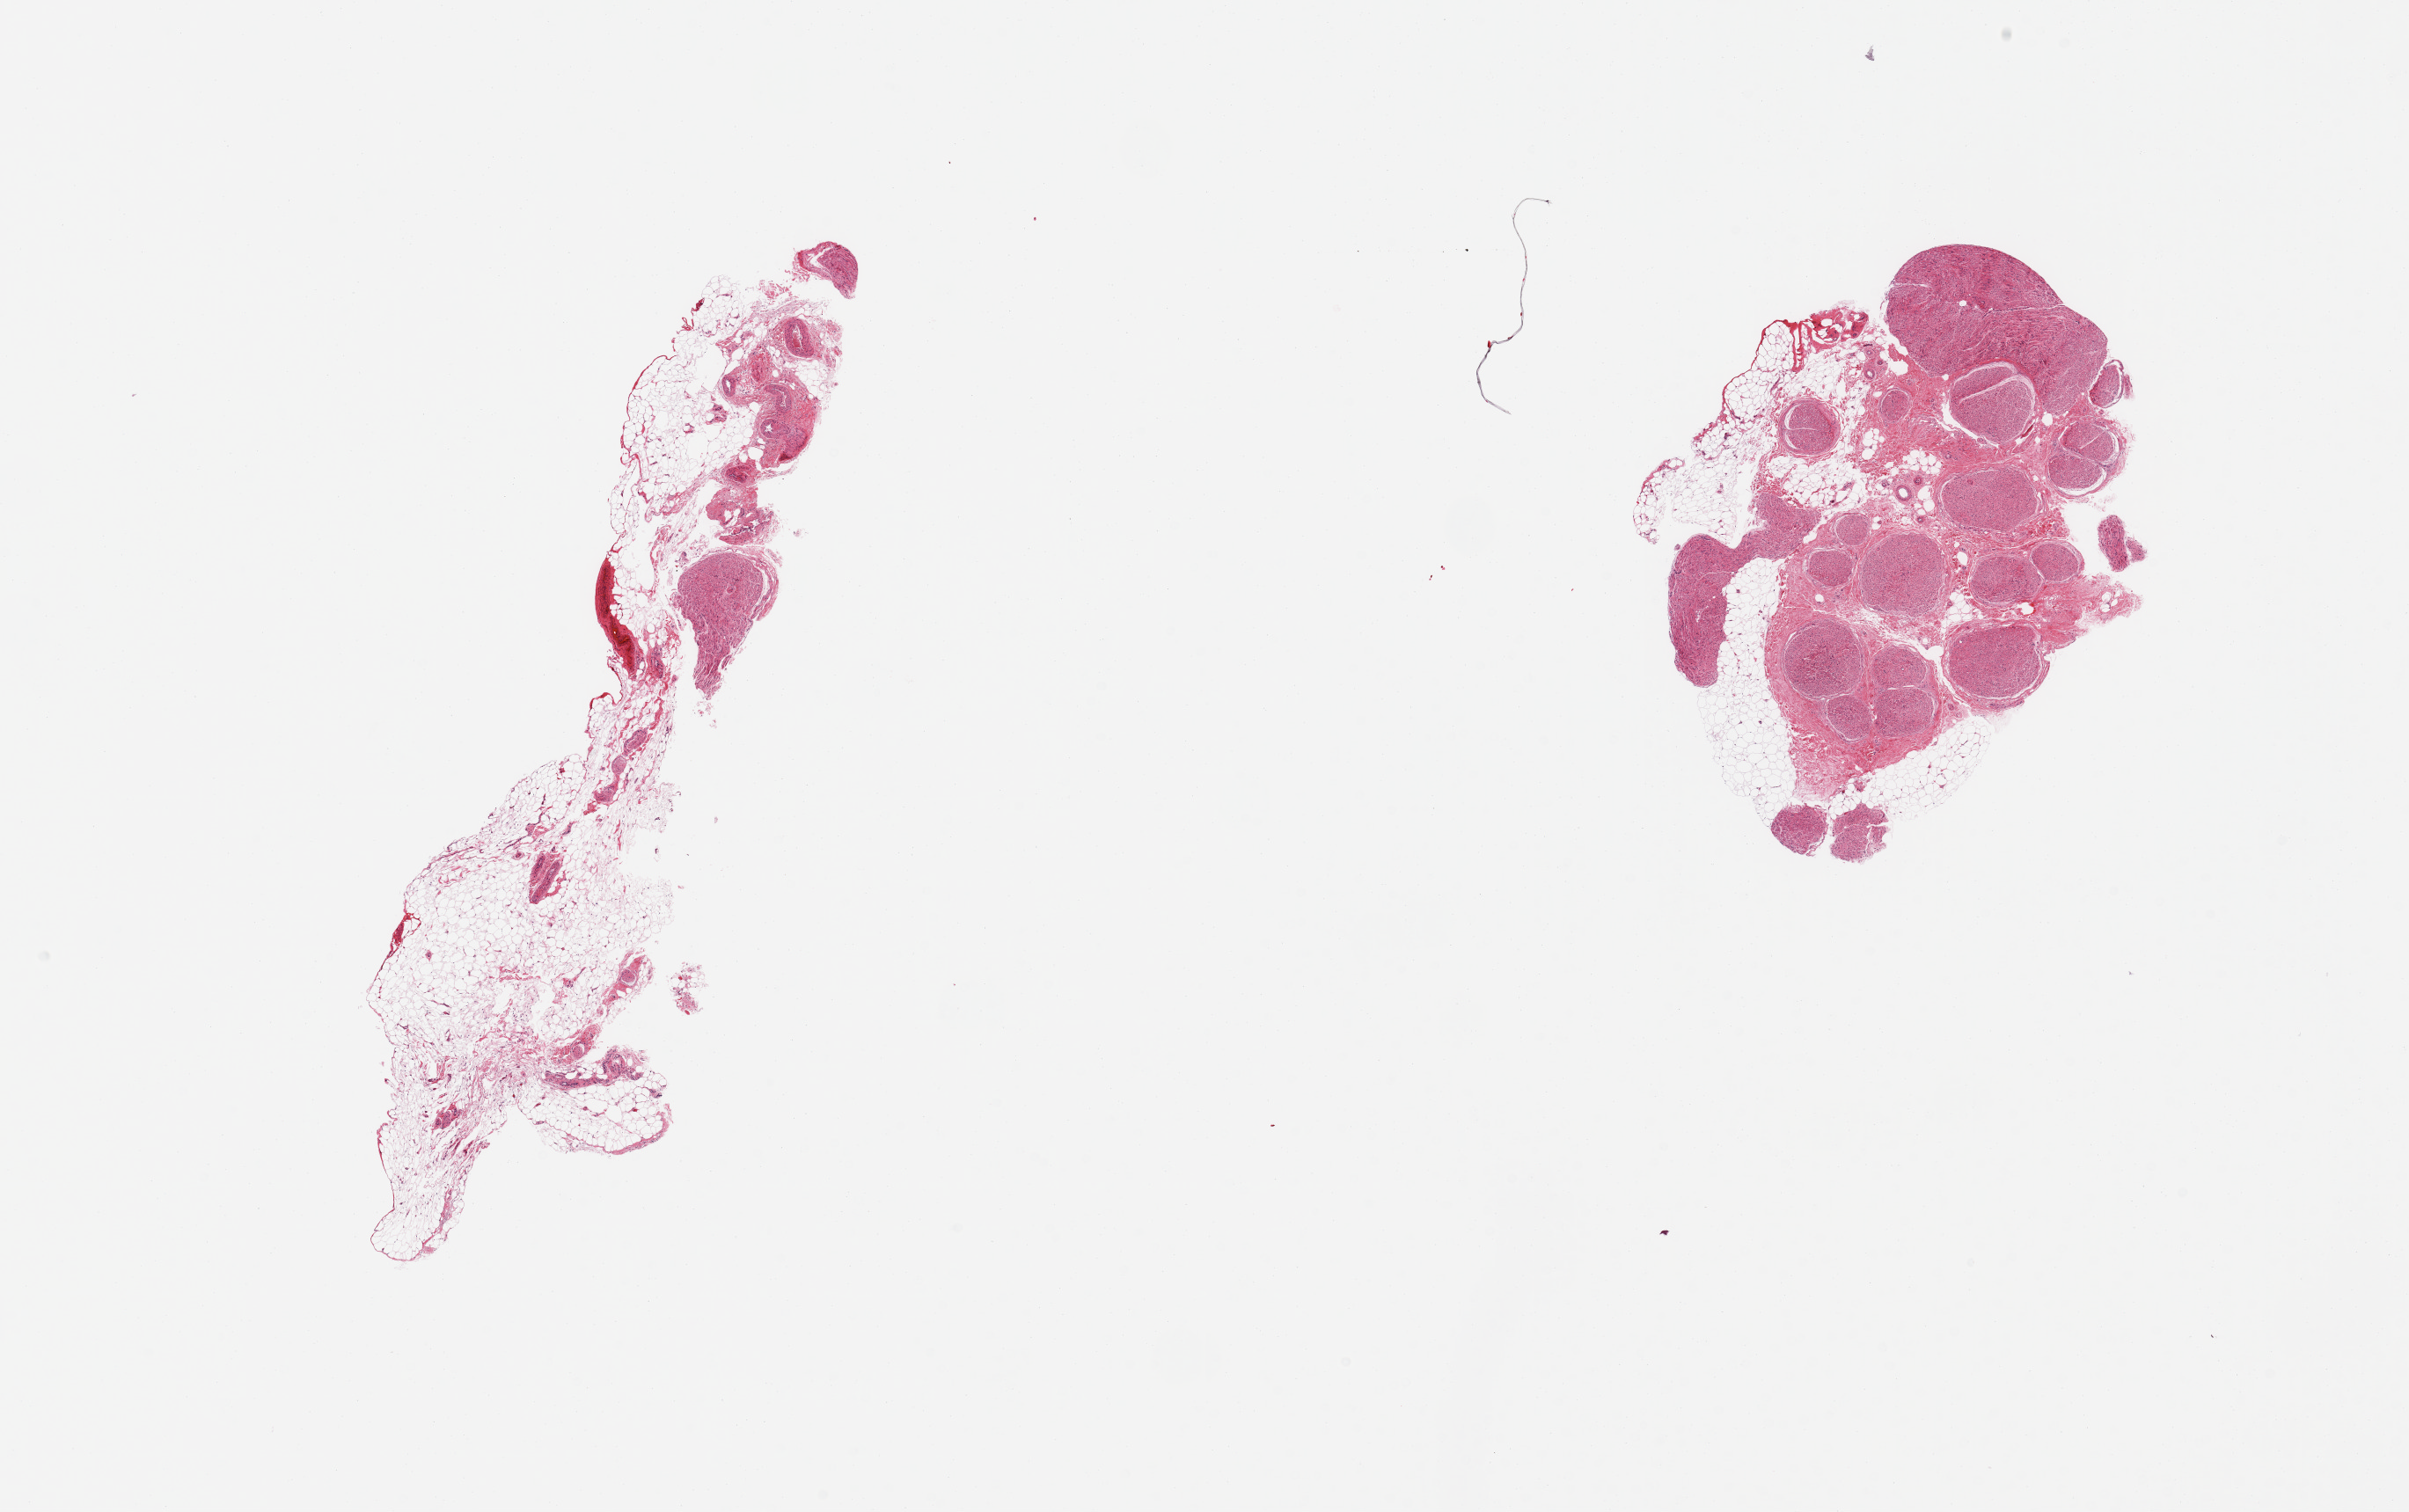
Whole-slide image, hematoxylin and eosin (H&E) stain, brightfield — a low-resolution overview of the entire scanned area, about 21.7 x 13.6 mm, PAXgene-fixed paraffin-embedded (PFPE) section, target tissue: tibial nerve, donor tissue sample. Donor sex: male.
Pathologist's review note for this sample: 2 pieces; 1 is 30% fat, 2nd is ~90% fat/vessels.